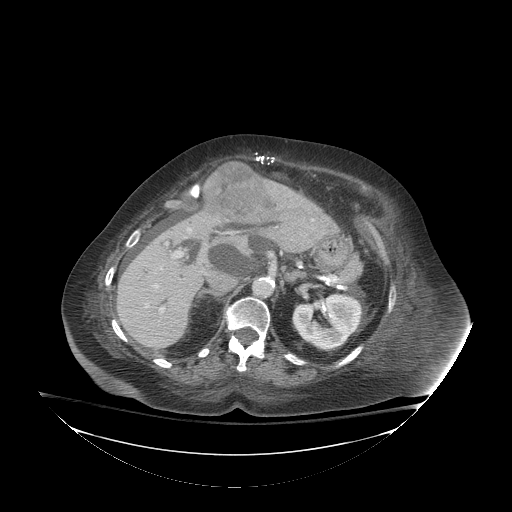
Contrast-enhanced abdominal CT (liver protocol), one axial slice; position 50 of 81 along the scan axis; soft-tissue window (W 400 / L 40 HU); 2.5 mm slice thickness; 512 × 512 image matrix, field of view 500 × 500 mm. Case-level facts recorded for this patient, not image findings: diagnosis: hepatocellular carcinoma (patient treated with transarterial chemoembolisation; whether this scan precedes or follows treatment is not stated here); TNM stage (as recorded): Stage-I.
Structures marked on this image (semi-automatically segmented with operator editing):
- liver parenchyma outside the tumour (the mass and vessels are separate outlines, so this box may not span the whole liver): box from (x=116, y=180) to (x=332, y=348) px
- mass: (x=204, y=161)–(x=275, y=224)
- liver vessels: (x=146, y=228)–(x=191, y=312)